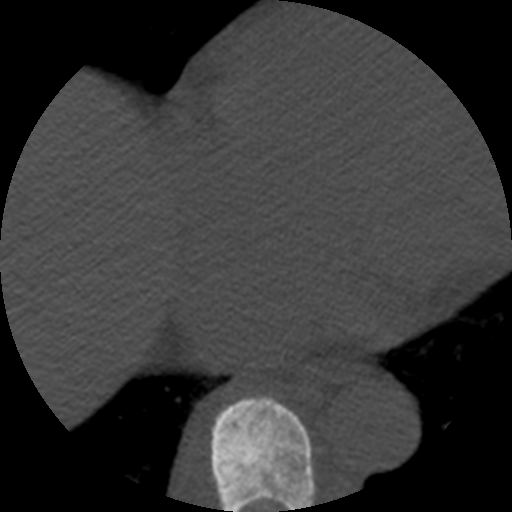
CT including the spine, one axial slice. Bone window (W 1800 / L 400 HU). 1.25 mm slice thickness. 512 × 512 image matrix, field of view 160 × 160 mm. Patient age 57 years. Case-level facts recorded for this patient, not image findings: primary cancer: prostate.
Outlined on this slice (semi-automatic segmentation, software-assisted and operator-edited):
- T8 vertebra: box from (x=210, y=397) to (x=317, y=512) px